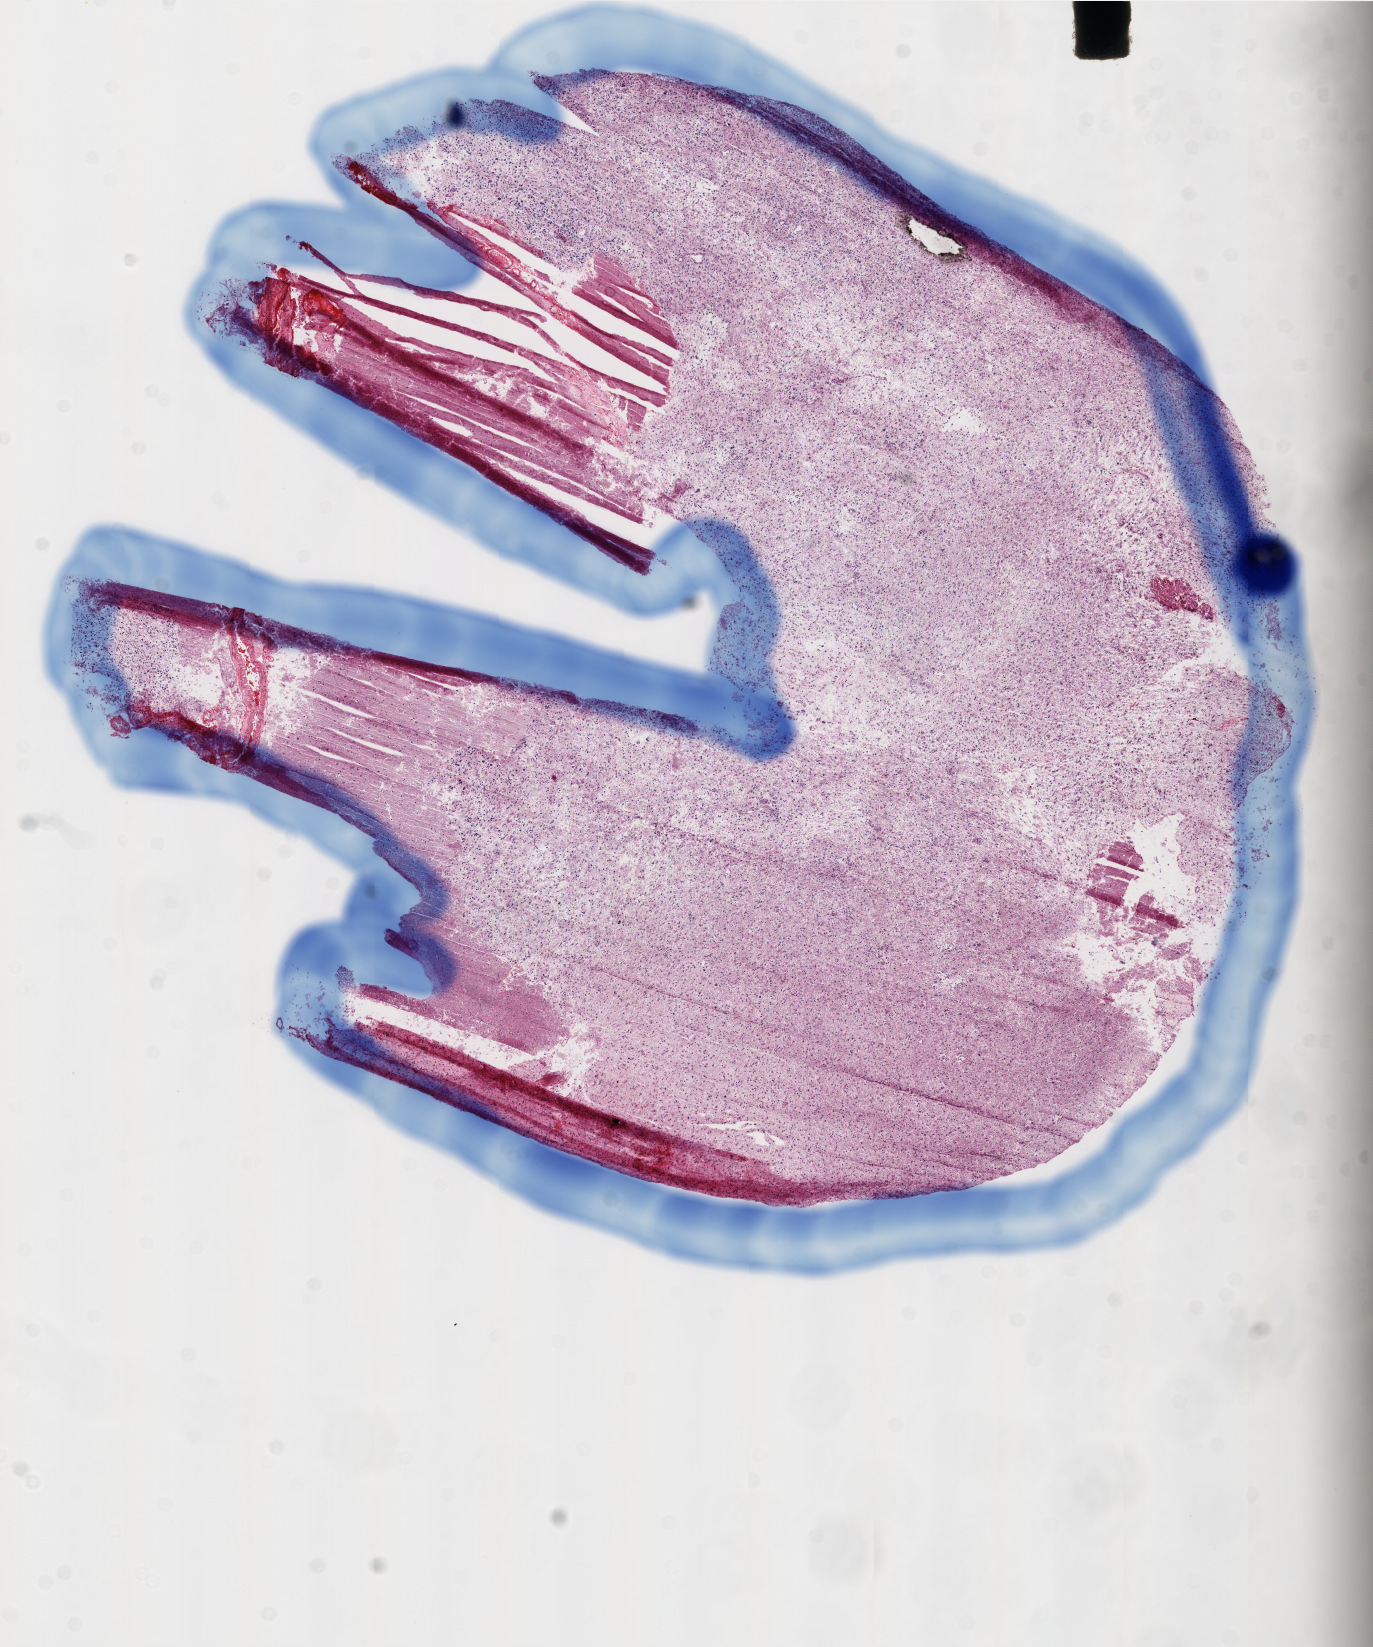
Digitized Hematoxylin and eosin (H&E) stained tissue section (whole slide), whole scanned area (about 11.0 x 13.2 mm, from a 20x scan) shown as a low-resolution overview. Frozen section from the top of the tissue portion. Sample: primary tumour, brain. Male patient; age at initial diagnosis 71 years. Pathologist review of this section (percent, as recorded): tumour cells 80%, tumour nuclei 95%, normal cells 0%, stromal cells 10%, necrosis 10%.
- histologic diagnosis: Glioblastoma